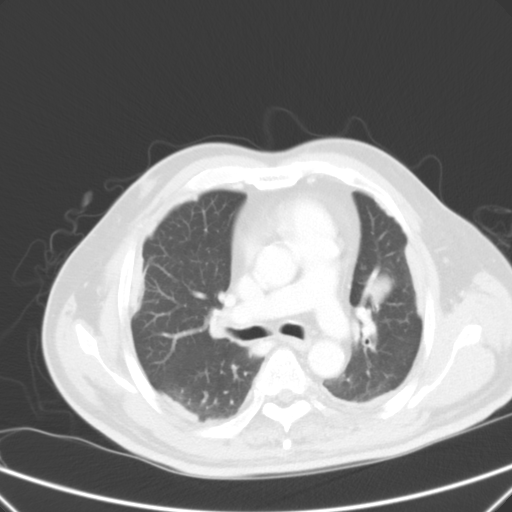
Chest CT, one axial slice; intravenous contrast given; lung window (W 1500 / L -600 HU); 5 mm slice thickness; 512 × 512 image matrix, field of view 357 × 357 mm. Patient: male, 66 years. From the clinical record (not read from this slice): clinical TNM (as recorded): T1c N3 M1a.
Structures marked on this image (bounding box drawn by a radiologist):
- lung tumour (recorded histology: squamous cell carcinoma): box from (x=358, y=262) to (x=395, y=311) px